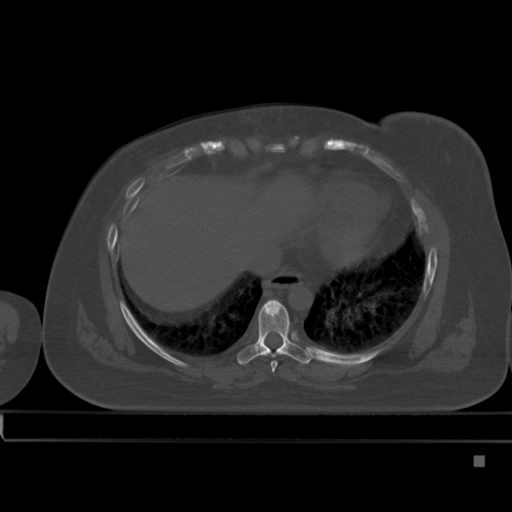
CT including the spine, one axial slice. Bone window (W 1800 / L 400 HU). 512 × 512 image matrix. Patient: female, 33 years. Case-level facts recorded for this patient, not image findings: primary cancer: breast; vertebrae with lytic lesions (as recorded): T1.
Outlined on this slice (semi-automatic segmentation, software-assisted and operator-edited):
- T7 vertebra: bounding box (x1, y1, x2, y2) in pixels: (271, 361, 278, 372)
- T8 vertebra: (237, 299, 312, 365)